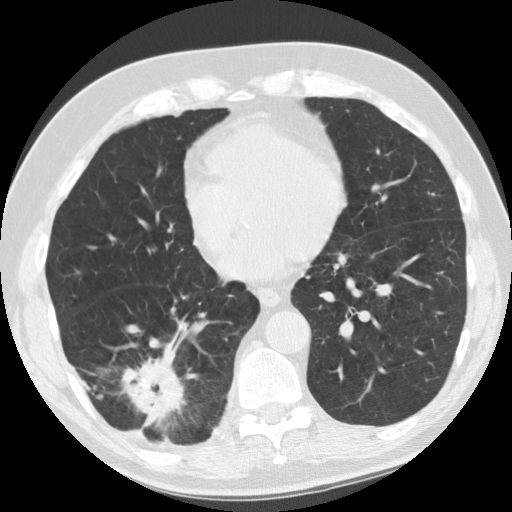
Low-dose screening chest CT, axial slice; baseline screening round; lung window (W 1500 / L -600 HU); 2.5 mm slice thickness; standard (soft-tissue) reconstruction kernel (STANDARD). Male, age 69 years at enrolment. Former smoker at enrolment.
Expert reader's lesion annotation, bounding box [x1, y1, x2, y2] px = [106, 331, 192, 440]. The screening reader recorded 2 non-calcified nodules or masses ≥4 mm on this exam (right lower lobe, right lower lobe); which of them this box marks is not recorded. Official screen result: positive, change unspecified: nodule(s) >= 4 mm or enlarging nodule(s), mass(es), or other non-specific abnormalities suspicious for lung cancer. Later outcome: lung cancer diagnosed 40 days after this screen — adenocarcinoma, NOS, right lower lobe, stage IIB (AJCC 6th edition), 45 mm at pathology.